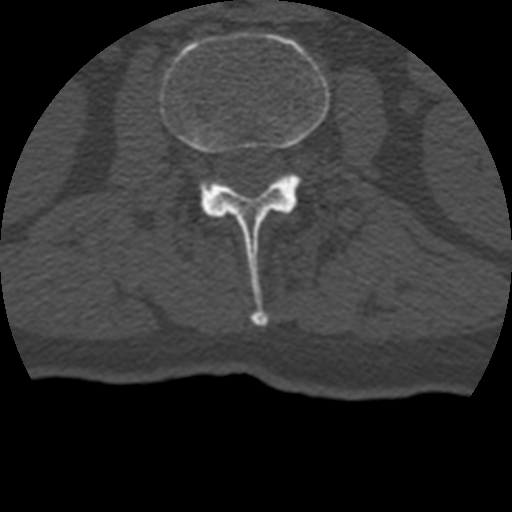
CT including the spine, one axial slice. Position 114 of 399 along the scan axis. Reconstruction kernel STANDARD. 120 kVp. Bone window (W 1800 / L 400 HU). 512 × 512 image matrix, field of view 160 × 160 mm. Patient age 69 years. From the clinical record (not read from this slice): primary cancer: prostate.
Outlined on this slice (semi-automatic segmentation, software-assisted and operator-edited):
- L2 vertebra: bounding box (x1, y1, x2, y2) in pixels: (159, 32, 330, 327)